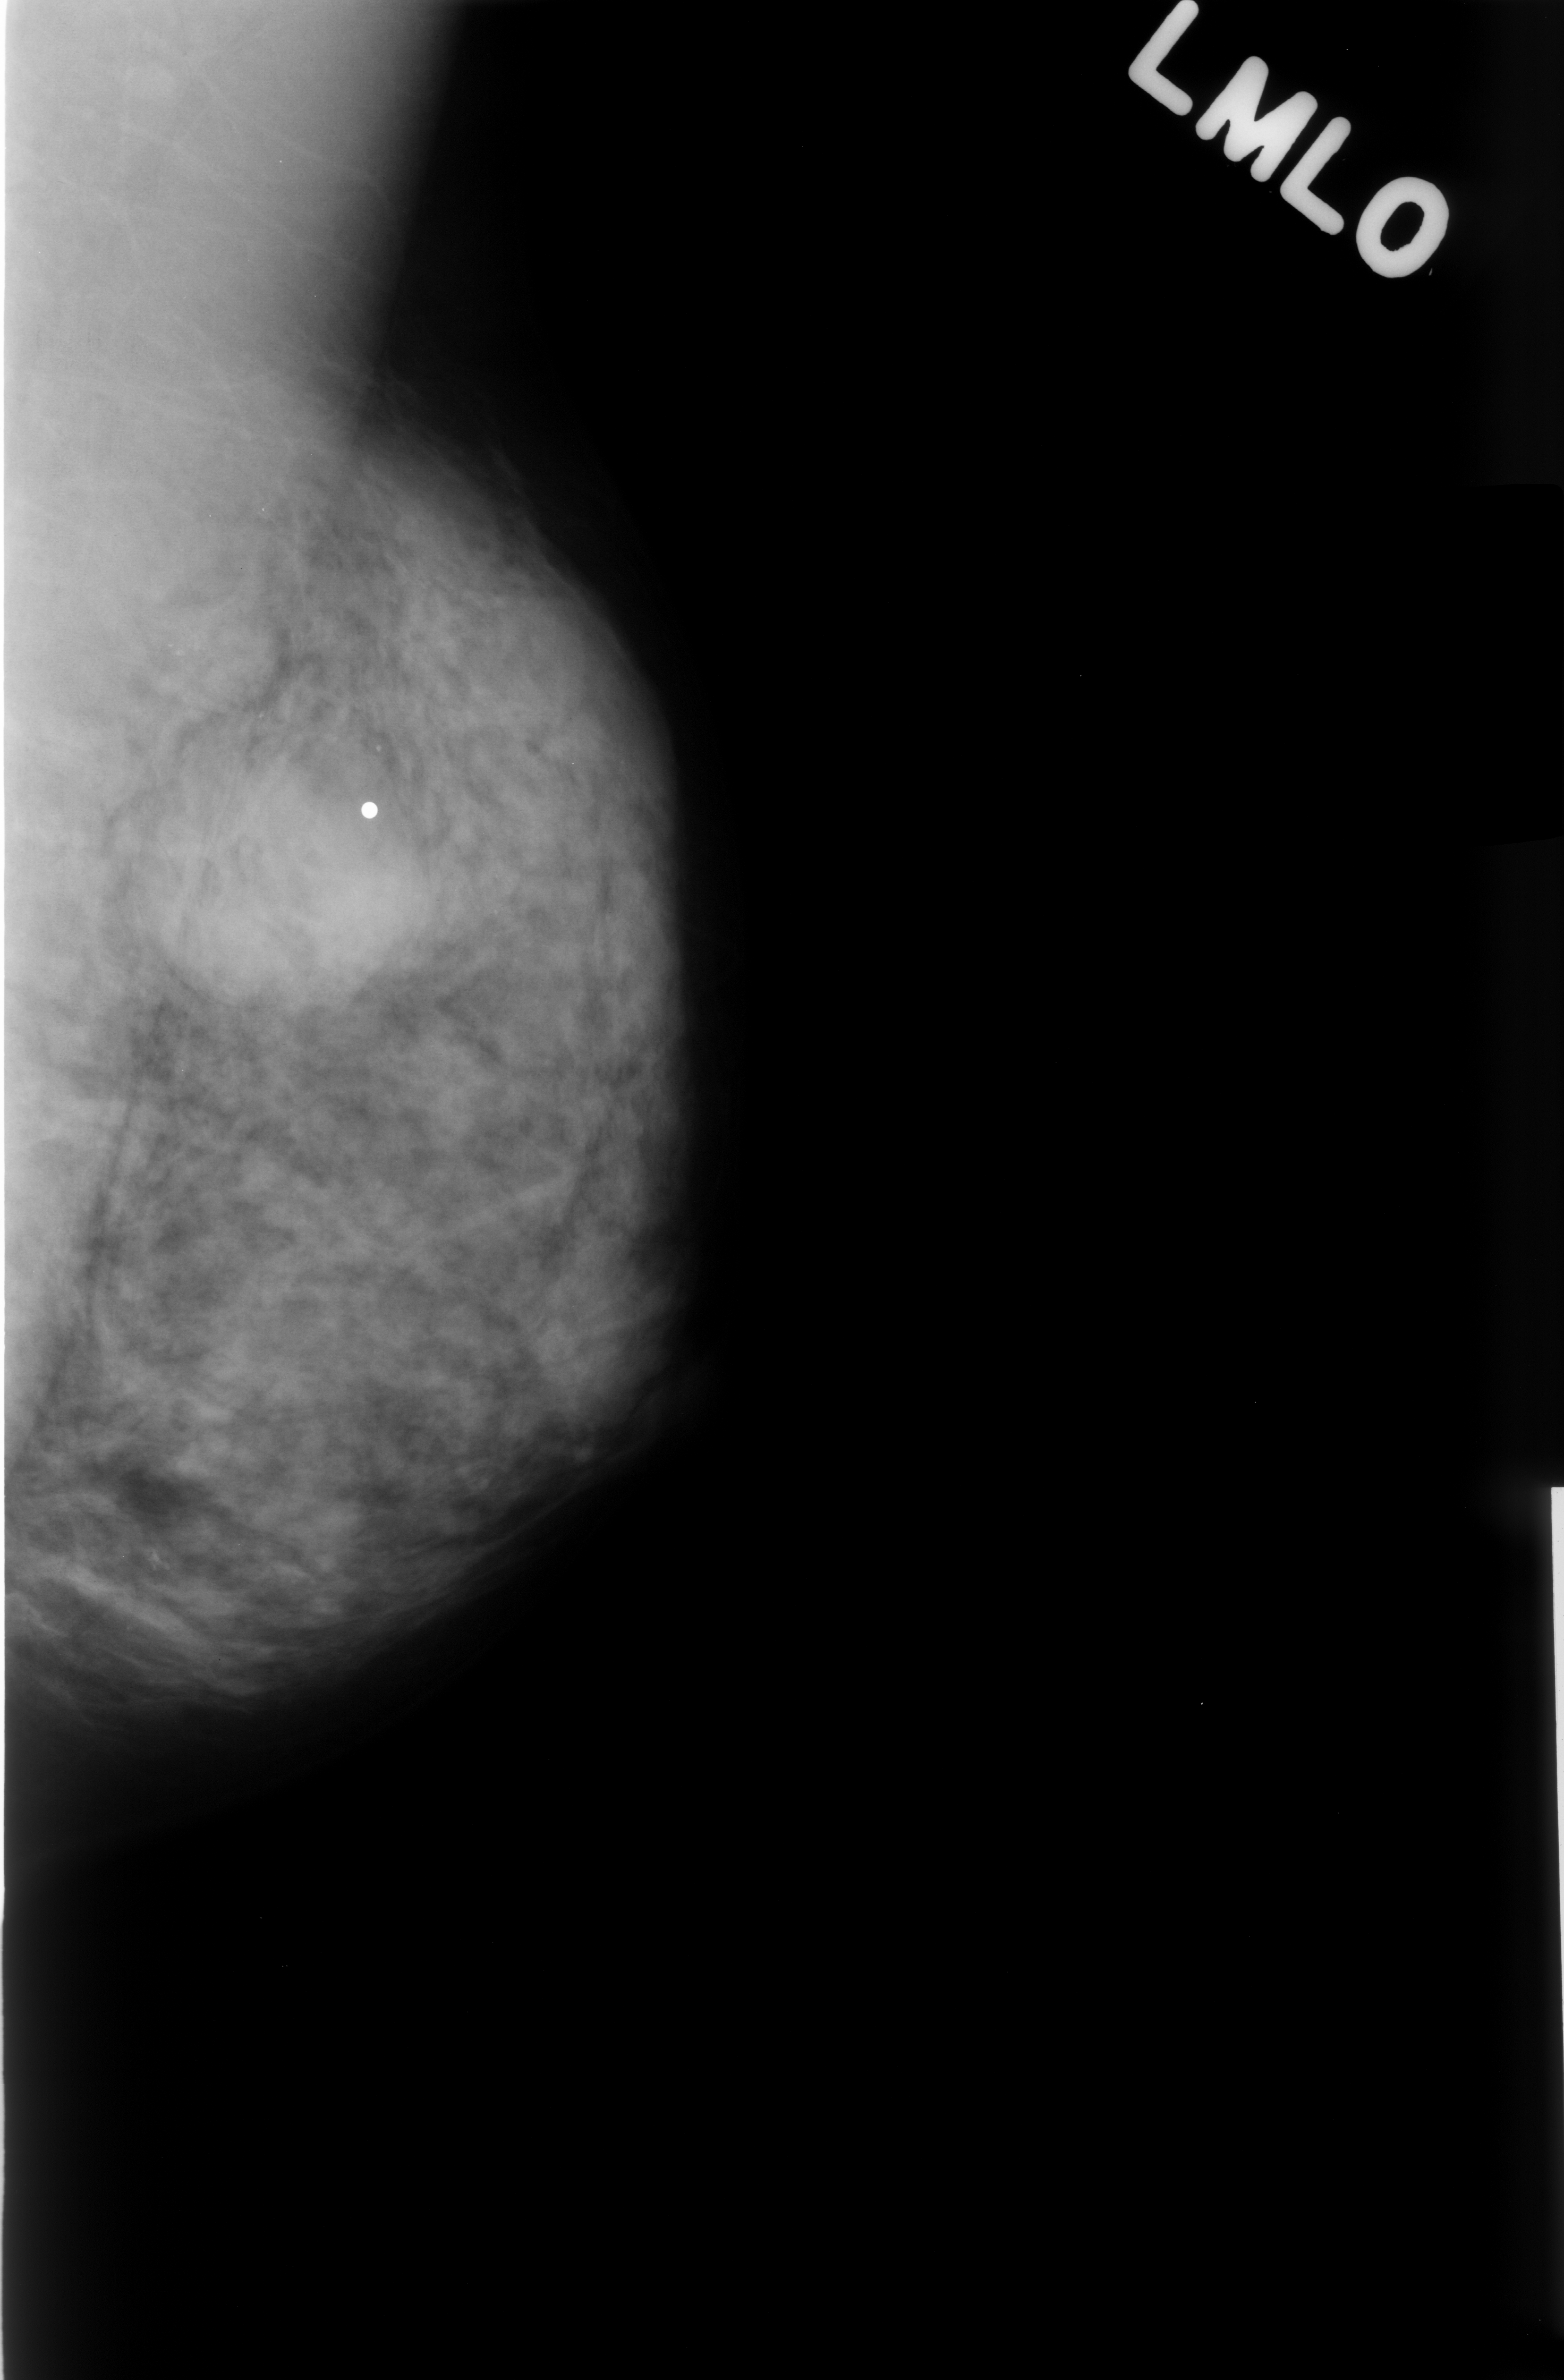
Mammogram (digitized film); left breast; MLO view; BI-RADS breast density category 3 (scale 1–4).
Marked abnormality: calcifications, morphology dystrophic, distribution clustered; BI-RADS assessment category 3; pathology result (as recorded, not read from the image): benign.